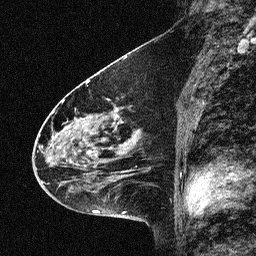
Breast MRI (dynamic contrast-enhanced), one sagittal slice. Slice 29 of 64 in the series (ordered by position). Dynamic contrast-enhanced study with each time point stored as its own series, time point 2 of 3 at this slice position (early post-contrast, ordered by acquisition time). 1.5 T. TE 4.5 ms, TR 11 ms. 256 × 256 image matrix, field of view 200 × 200 mm. Patient: female, 46 years. Case-level facts recorded for this patient, not image findings: setting: breast cancer imaged before/during neoadjuvant chemotherapy; receptor status: HER2-positive.
Structures marked on this image (semi-automatic segmentation, software-assisted and operator-edited):
- analysis volume of interest (the breast-tissue region the enhancement analysis was run in; not a lesion): bounding box <42,80,150,180> (left, top, right, bottom; pixels)
- tumour enhancement mask (voxels above the 90 % enhancement threshold inside the analysis volume of interest): <51,105,136,179>